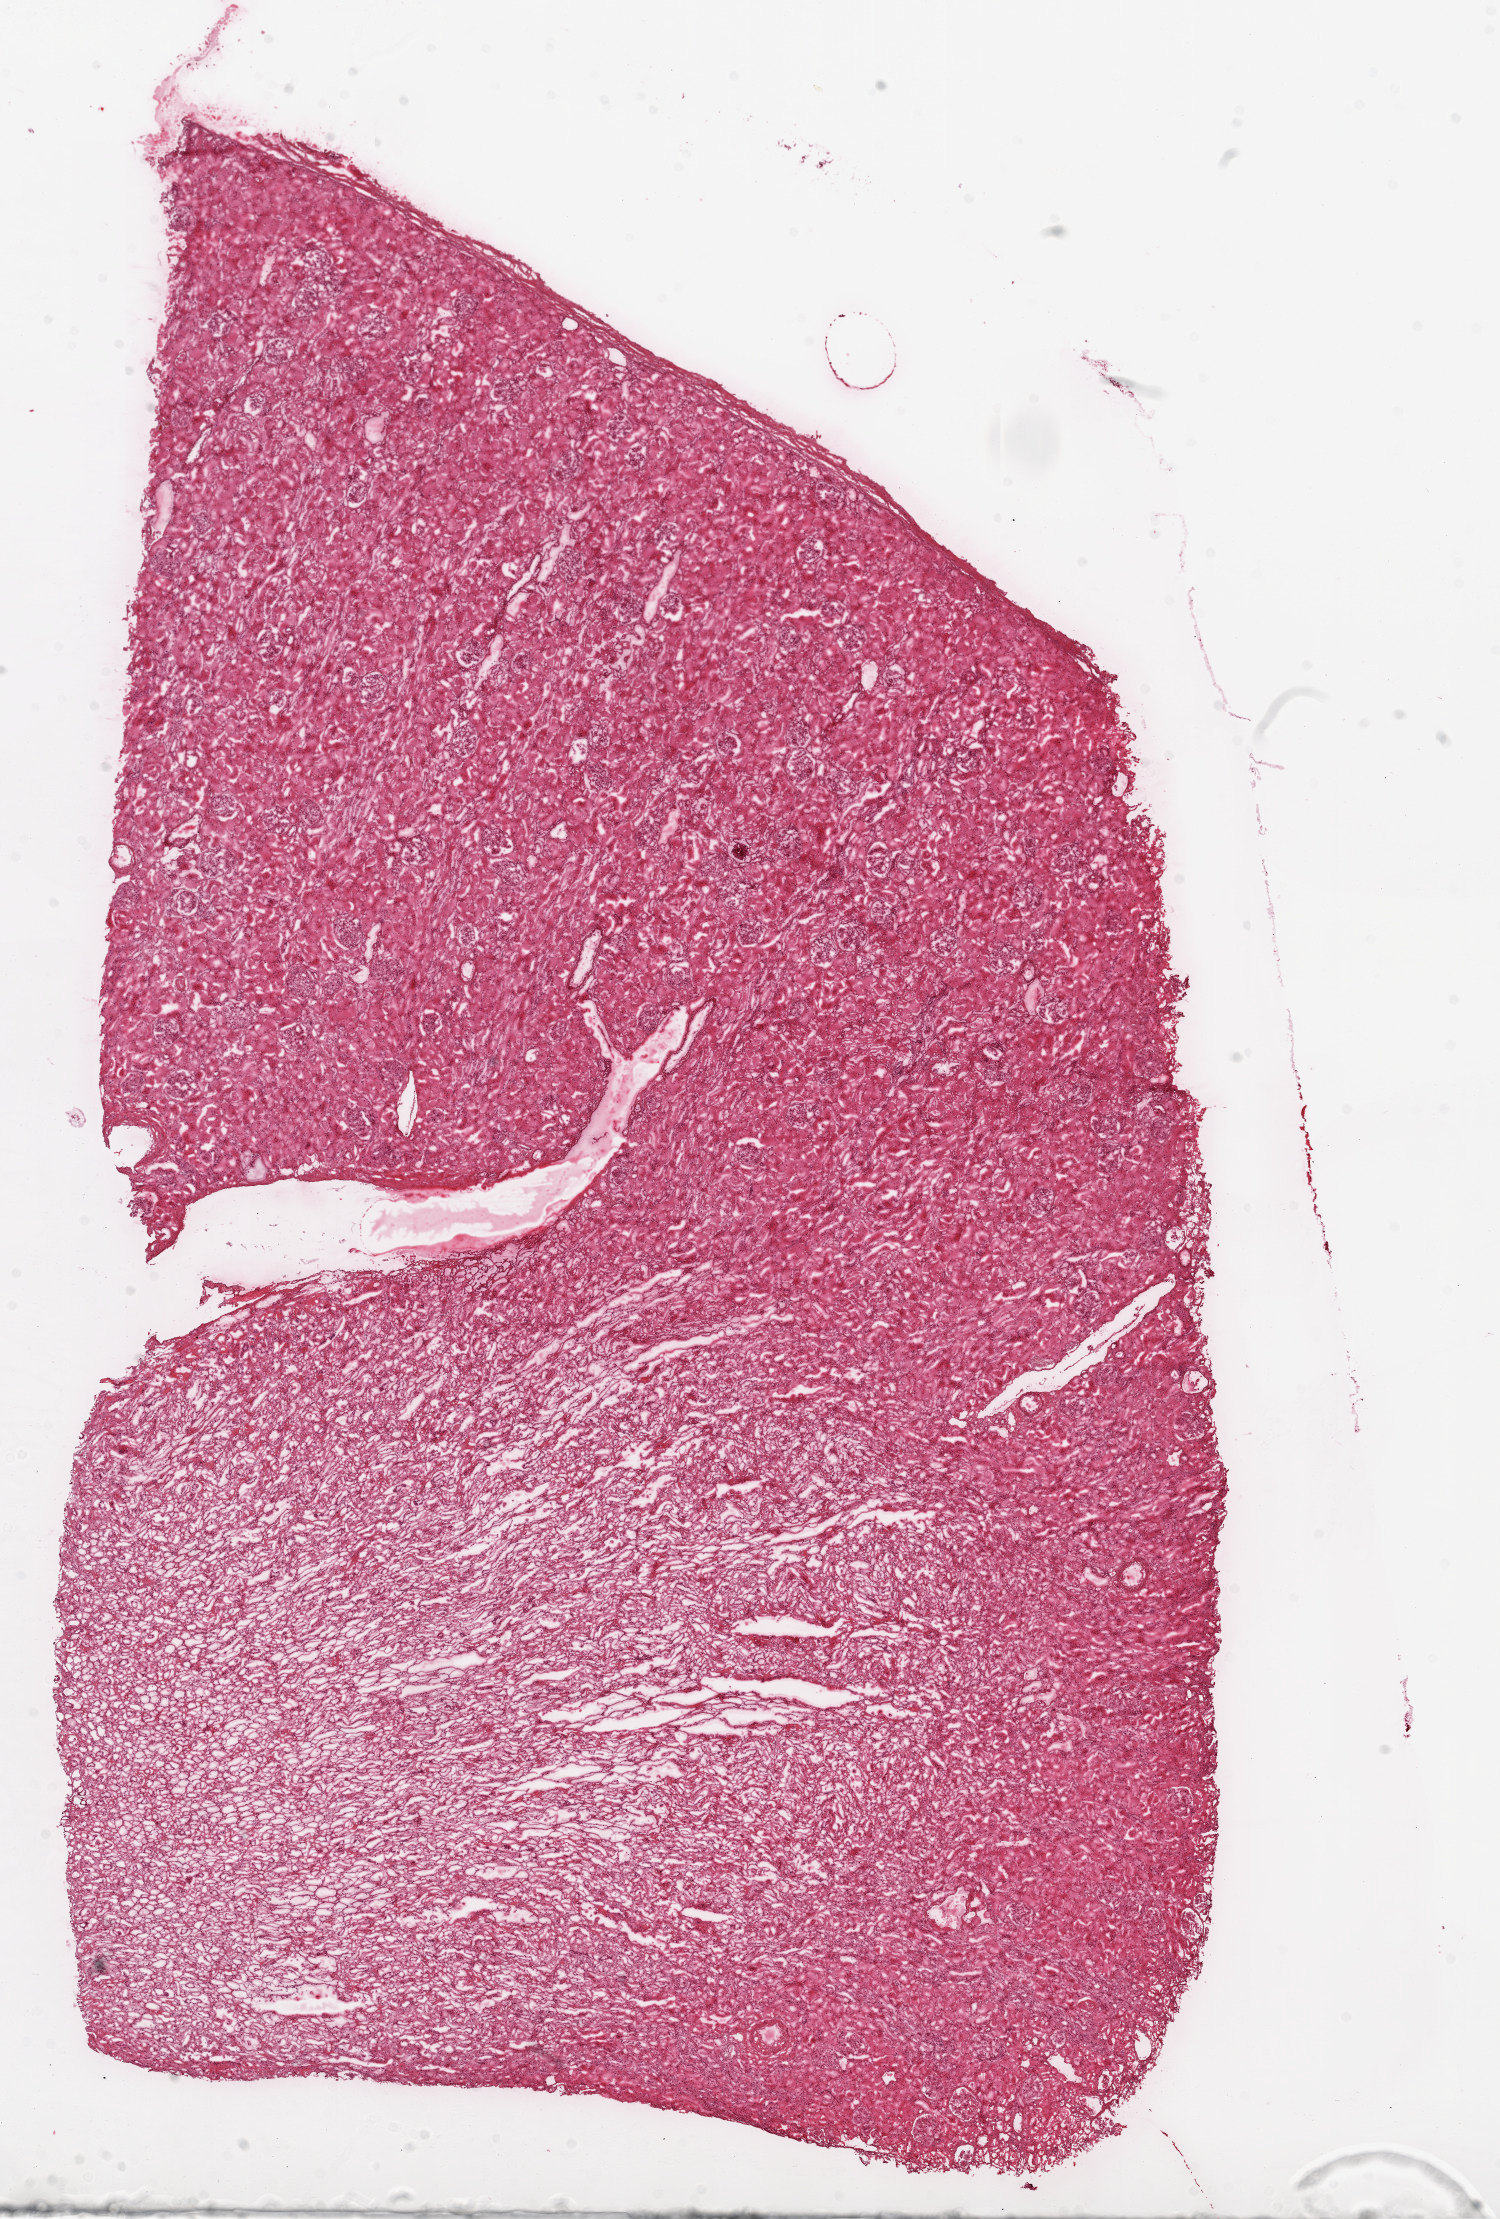
H&E whole-slide image, low-resolution overview of the scanned area, about 12.0 x 17.8 mm, frozen section, solid tissue normal (non-tumour tissue) sample from the kidney. Male patient; age at initial diagnosis 58 years.
This section: solid tissue normal sample (biorepository sample class). Patient diagnosis: Clear cell adenocarcinoma, NOS.